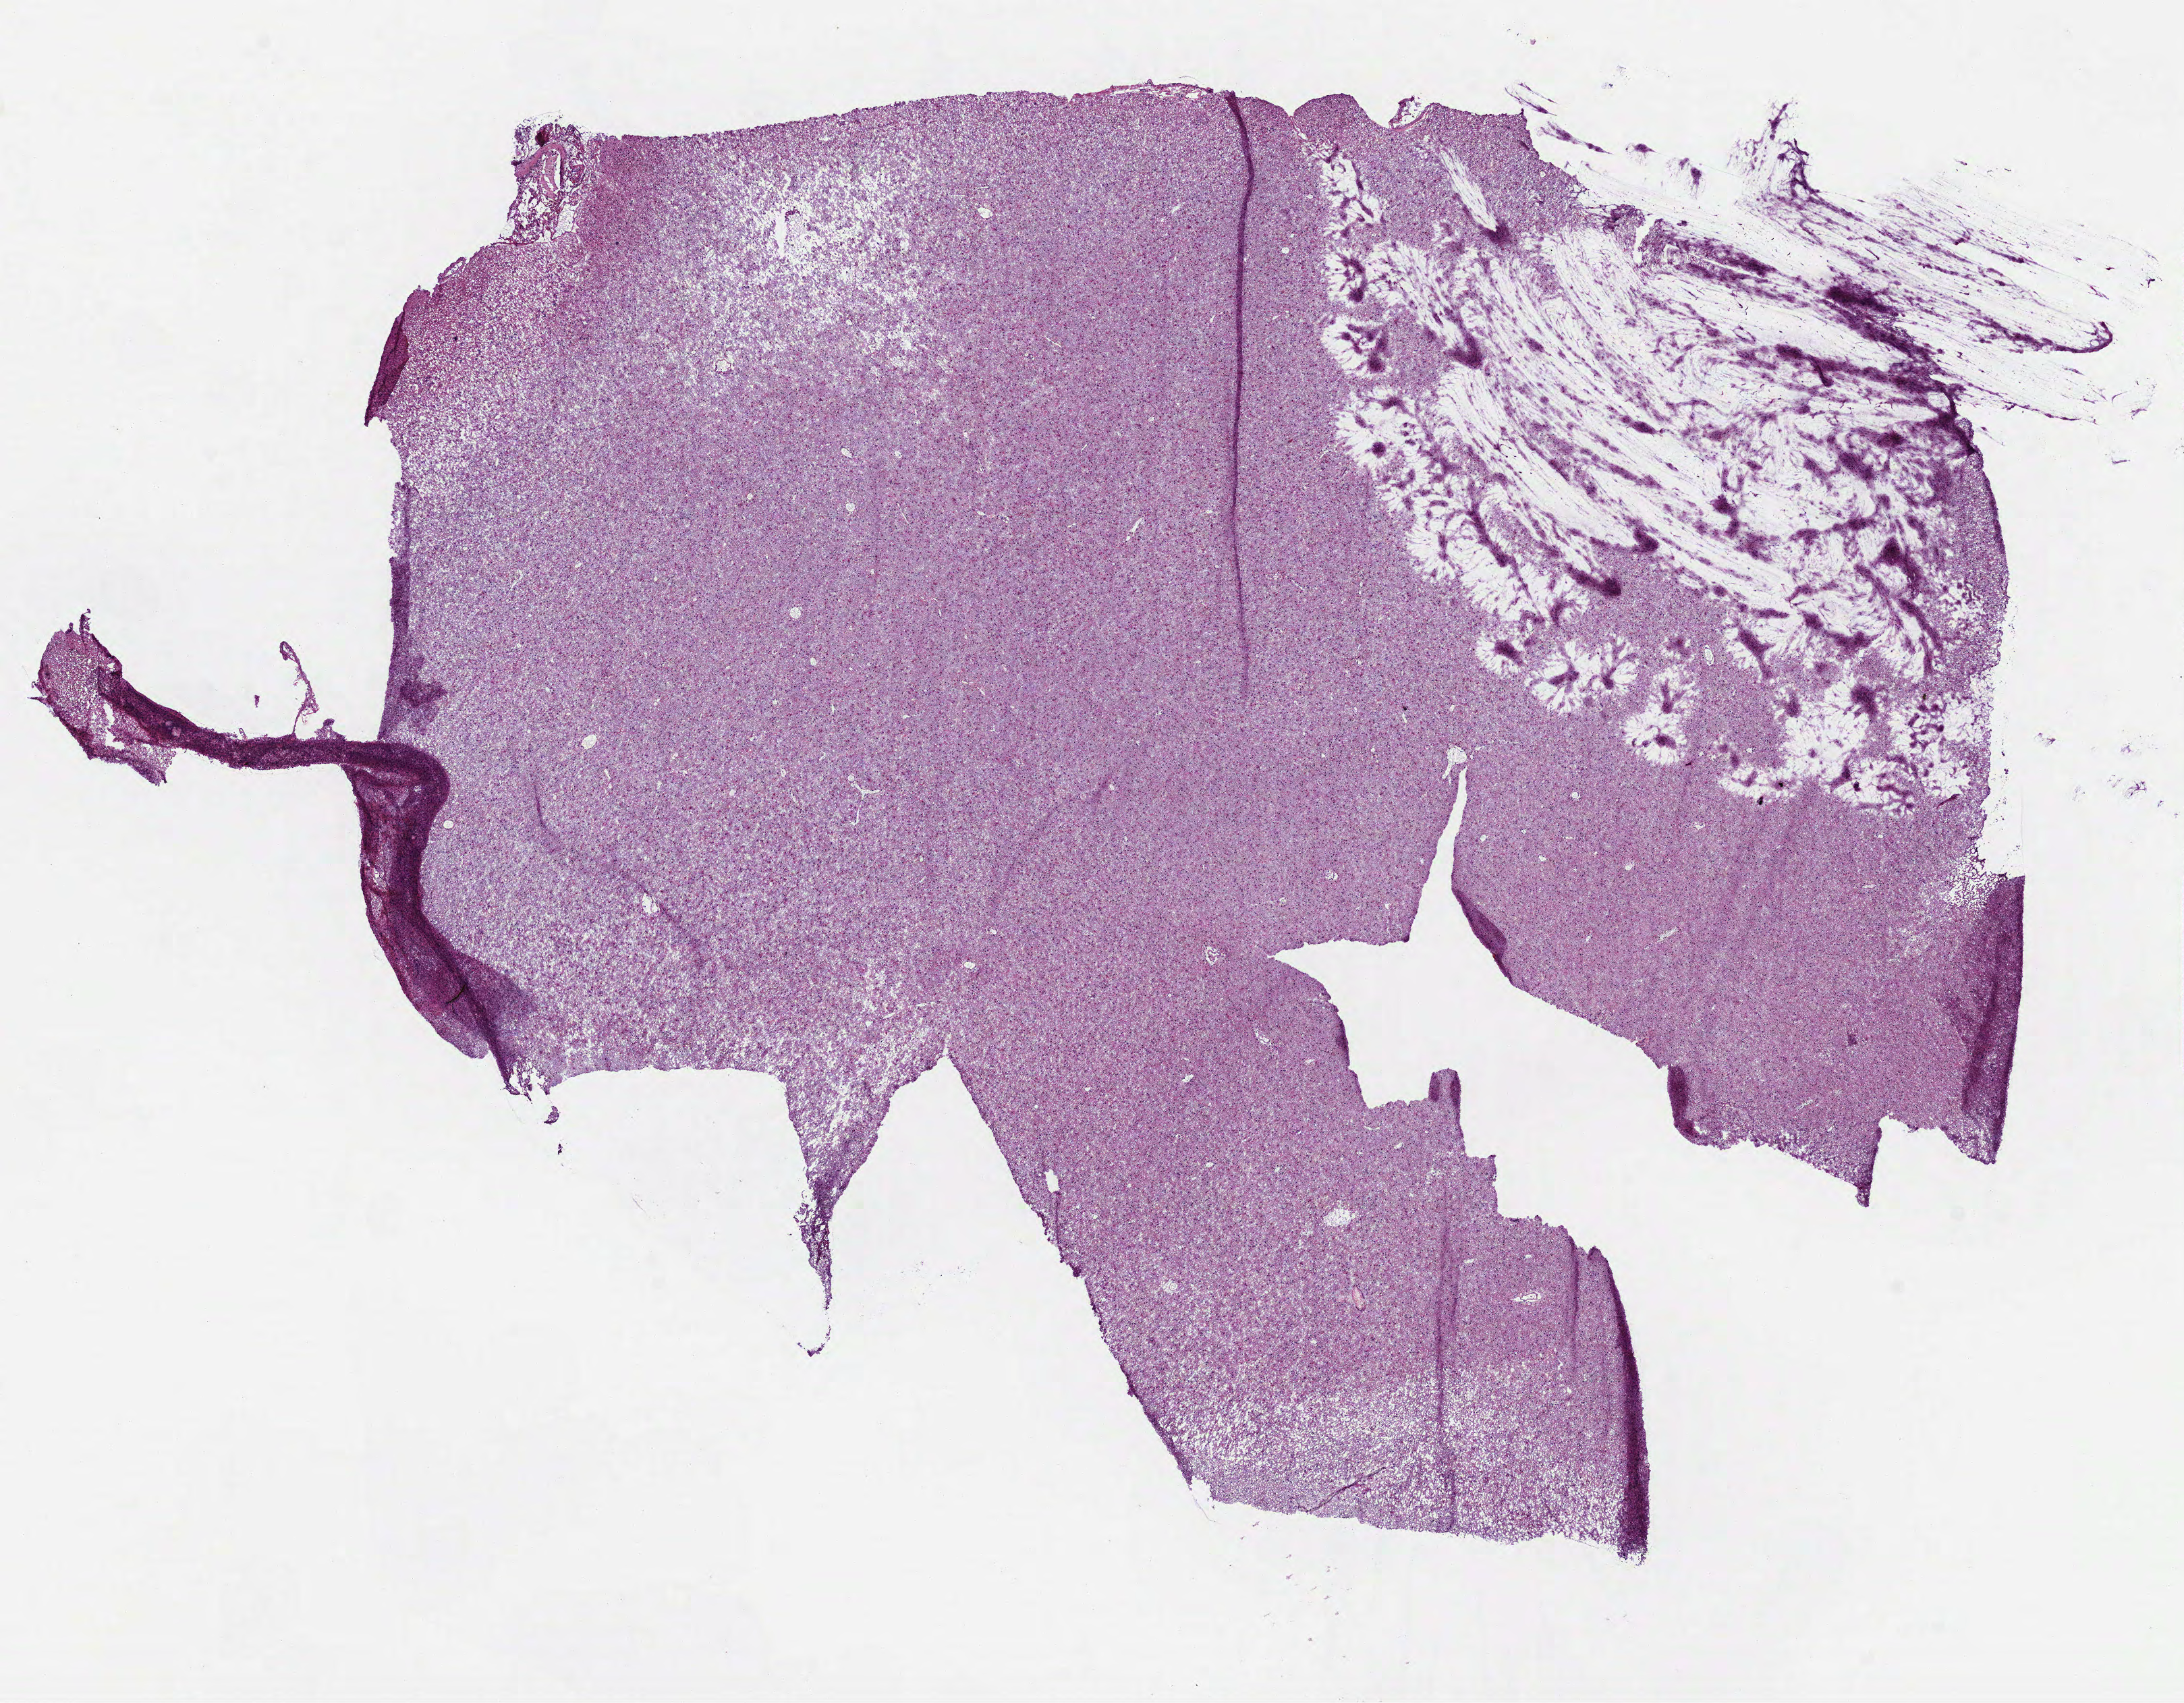
Digitized H&E-stained tissue section (whole slide), shown as a low-resolution overview of the whole scanned area (about 13.1 x 10.2 mm). Frozen section from the bottom of the tissue portion. Brain, primary tumour sample. Male patient; age at initial diagnosis 62 years. Histologic grade: G2 (moderately differentiated). Composition of this section per pathologist review: tumour cells 100%, tumour nuclei 70%, normal cells 0%, stromal cells 0%, necrosis 0%.
Diagnosis: Astrocytoma, NOS (cerebrum).